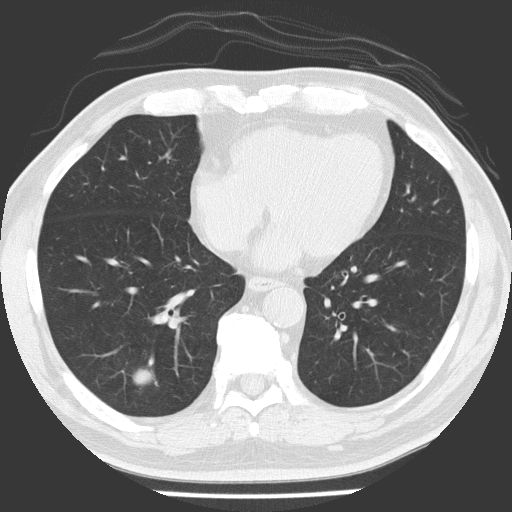
Low-dose screening chest CT, axial slice; baseline annual screen; lung window (W 1500 / L -600 HU); 2 mm slice thickness; lung (sharp) reconstruction kernel (FC51); 512 × 512 image matrix. Male participant, aged 56 years at enrolment. Former smoker at enrolment.
• Expert-annotated lung lesion, bounding box (x1, y1, x2, y2) in pixels: (107, 344, 164, 404).
• Screening reader's record for this exam (one nodule recorded; not confirmed to be the boxed lesion): non-calcified nodule or mass ≥4 mm, right lower lobe, 21 × 17 mm, spiculated (stellate) margins, soft tissue attenuation.
• Official screen result: positive, change unspecified: nodule(s) >= 4 mm or enlarging nodule(s), mass(es), or other non-specific abnormalities suspicious for lung cancer.
• Later outcome: lung cancer diagnosed 84 days after this screen — adenocarcinoma, NOS, right lower lobe, poorly differentiated (G3), stage IA (AJCC 6th edition), 24 mm at pathology.